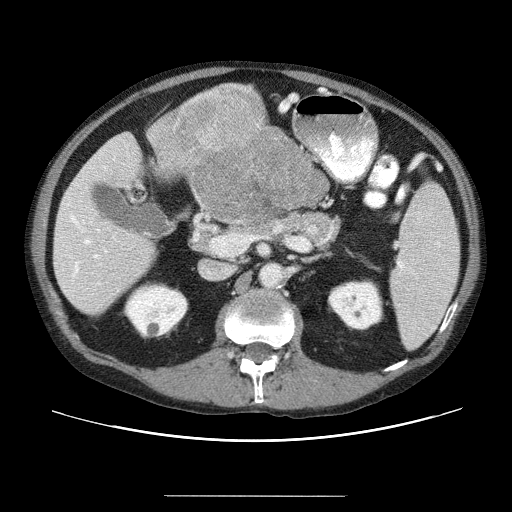
Contrast-enhanced abdominal CT (liver protocol), one axial slice. Slice 15 of 69 in the series (ordered by position). Soft-tissue window (W 400 / L 40 HU). 2.5 mm slice thickness. 512 × 512 image matrix. Case-level facts recorded for this patient, not image findings: diagnosis: hepatocellular carcinoma (patient treated with transarterial chemoembolisation; whether this scan precedes or follows treatment is not stated here); TNM stage (as recorded): Stage-IVB; Child-Pugh class: B.
Structures marked on this image (semi-automatic segmentation, software-assisted and operator-edited):
- liver parenchyma outside the tumour (the mass and vessels are separate outlines, so this box may not span the whole liver): bounding box (x1, y1, x2, y2) in pixels: (52, 136, 320, 308)
- mass: (149, 87, 328, 226)
- liver vessels: (58, 143, 127, 295)